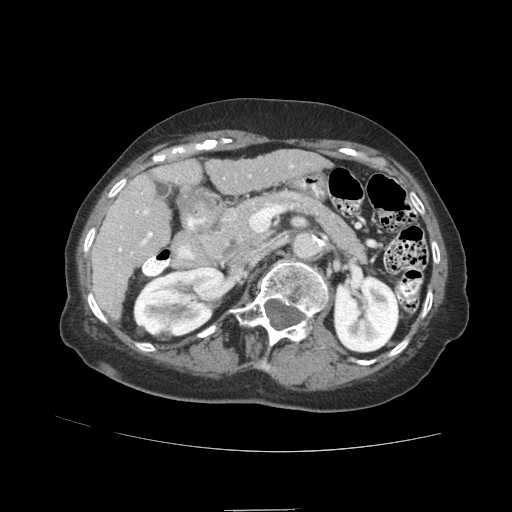
Contrast-enhanced abdominal CT (liver protocol), one axial slice; slice 40 of 89 in the series (ordered by position); reconstruction kernel STANDARD; soft-tissue window (W 400 / L 40 HU); 2.5 mm slice thickness; 512 × 512 image matrix, field of view 360 × 360 mm. Case-level facts recorded for this patient, not image findings: diagnosis: hepatocellular carcinoma (patient treated with transarterial chemoembolisation; whether this scan precedes or follows treatment is not stated here); TNM stage (as recorded): Stage-II; Child-Pugh class: A; tumour differentiation: moderately differentiated; tumour nodularity: multinodular.
Outlined on this slice (semi-automatic segmentation, software-assisted and operator-edited):
- liver parenchyma outside the tumour (the mass and vessels are separate outlines, so this box may not span the whole liver): bounding box [x1, y1, x2, y2] px = [90, 150, 327, 318]
- liver vessels: [110, 165, 294, 277]